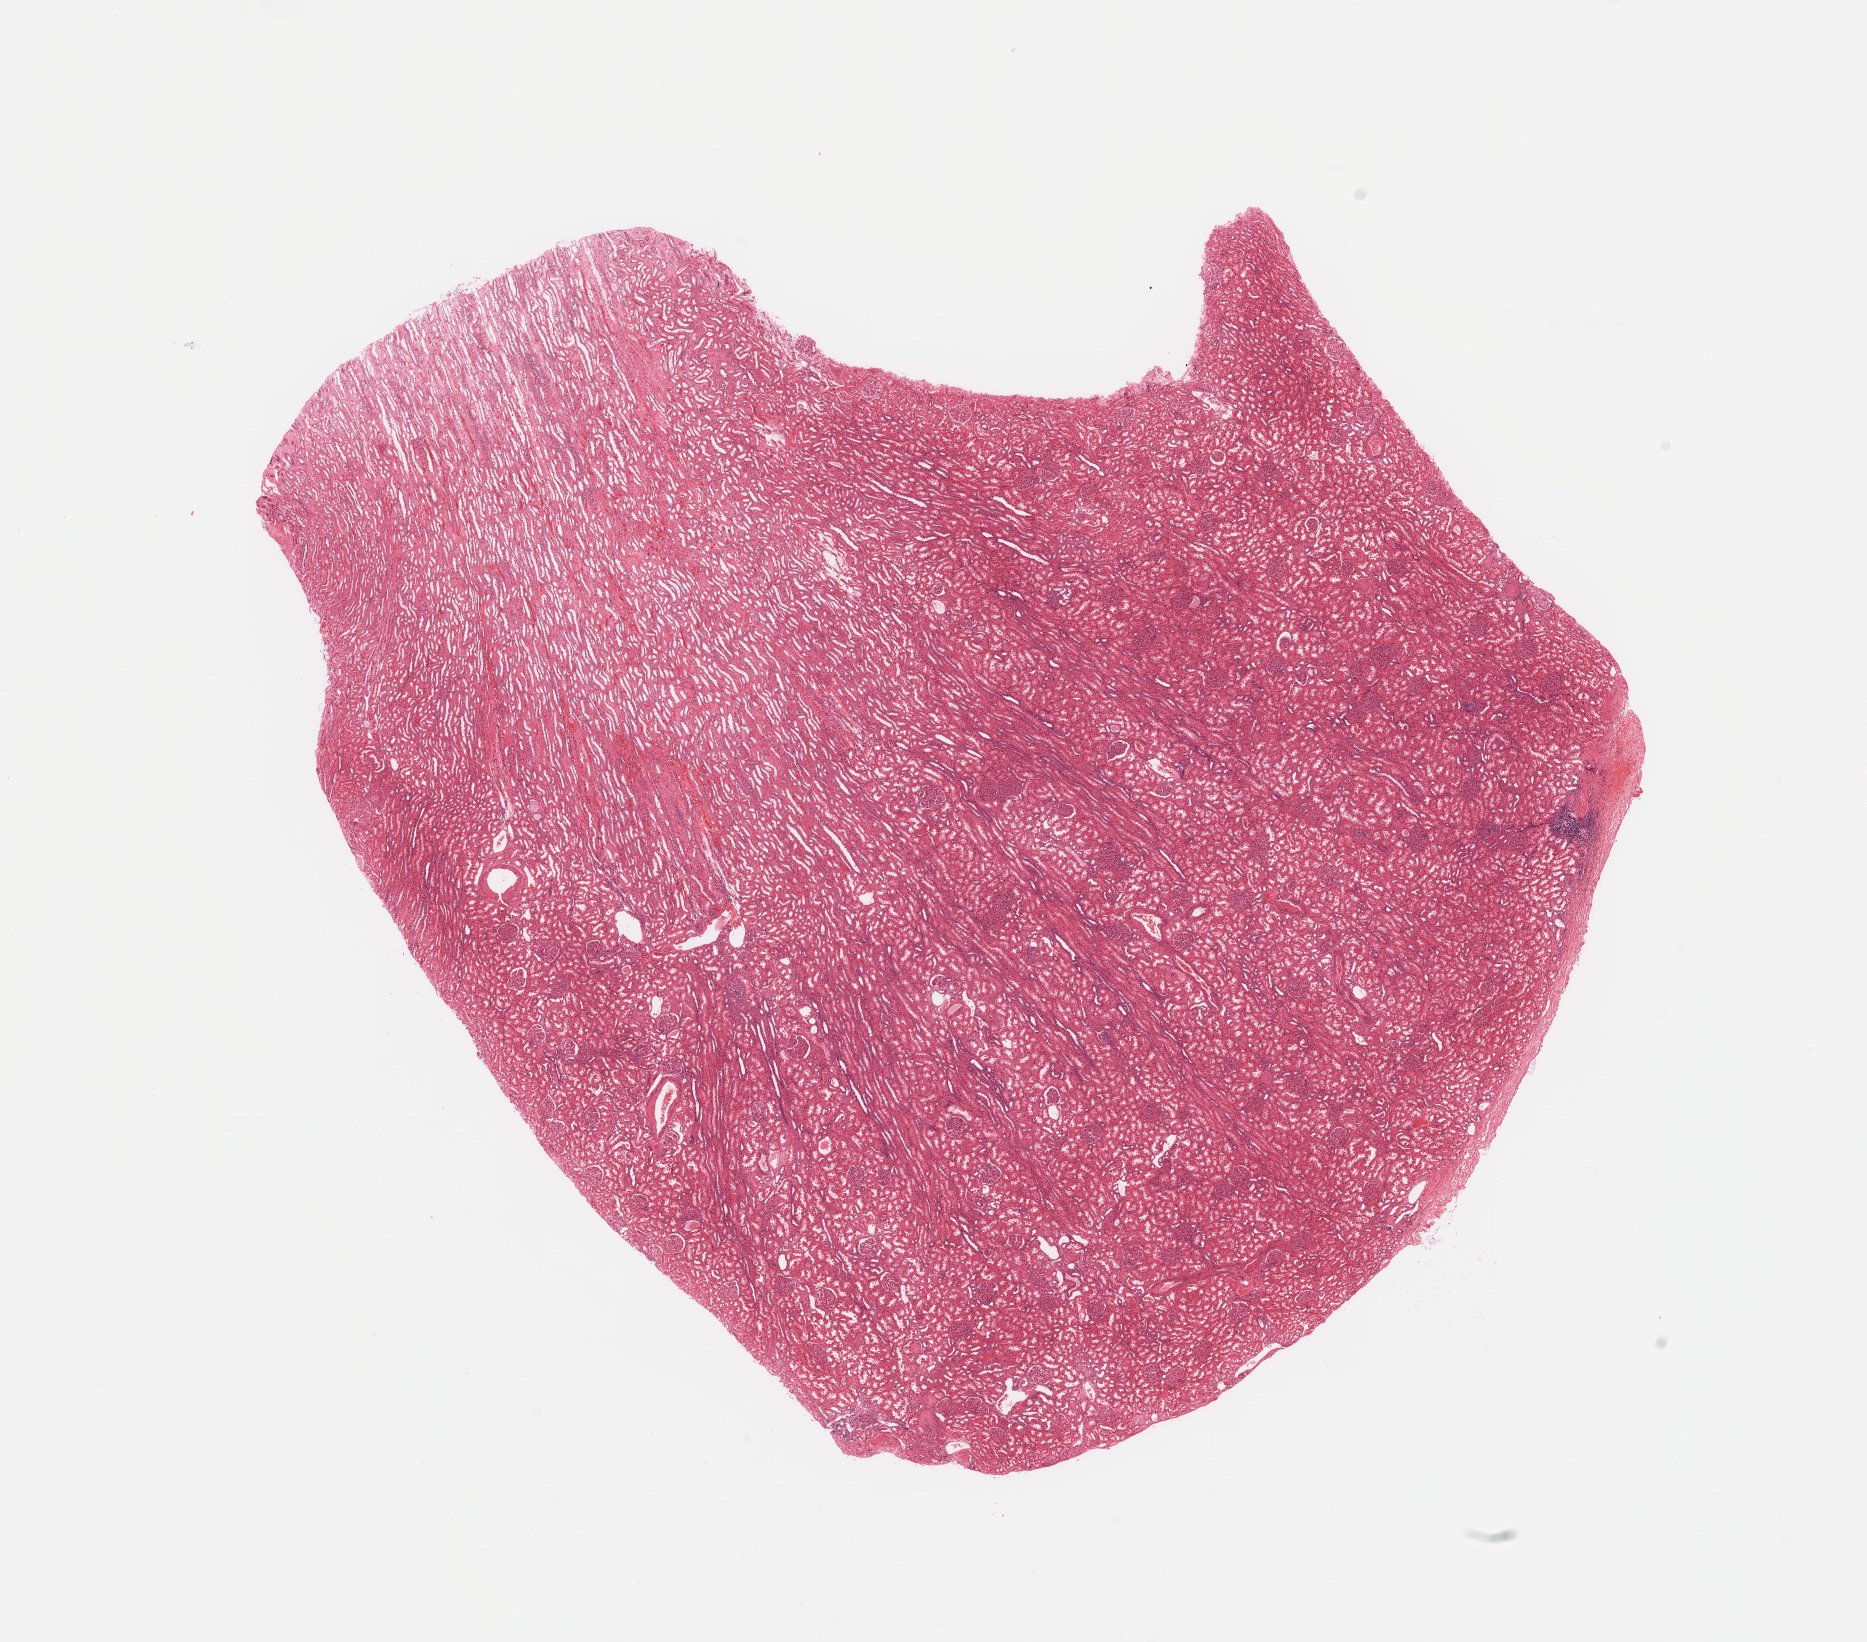
H&E whole-slide image, whole scanned area (about 14.8 x 13.0 mm, slide scanned at 20x) shown as a low-resolution overview; kidney, normal (non-tumour) tissue. Male, 61 y/o.
This section: normal (non-tumour) tissue from the same patient. Patient diagnosis: Renal cell carcinoma, NOS.